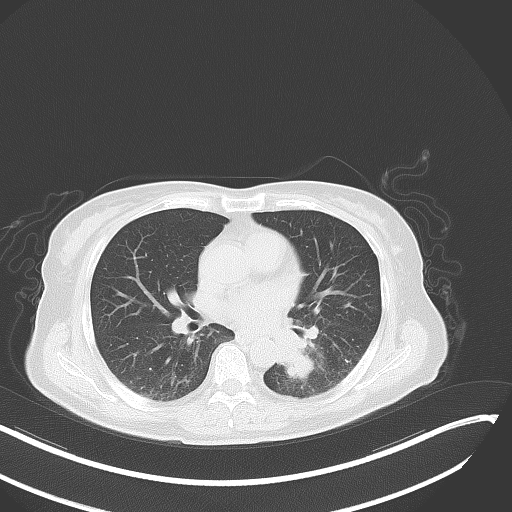
Chest CT, one axial slice. Position 19 of 48 along the scan axis. Reconstruction kernel B70f. 120 kVp. Lung window (W 1500 / L -600 HU). 5 mm slice thickness. 512 × 512 image matrix, field of view 400 × 400 mm. Female patient, age 64 years. From the clinical record (not read from this slice): clinical TNM (as recorded): T3 N1 M1; histopathological grade: G3.
Outlined on this slice (bounding box drawn by a radiologist):
- lung tumour (recorded histology: small cell carcinoma): bounding box (x1, y1, x2, y2) in pixels: (270, 320, 323, 380)